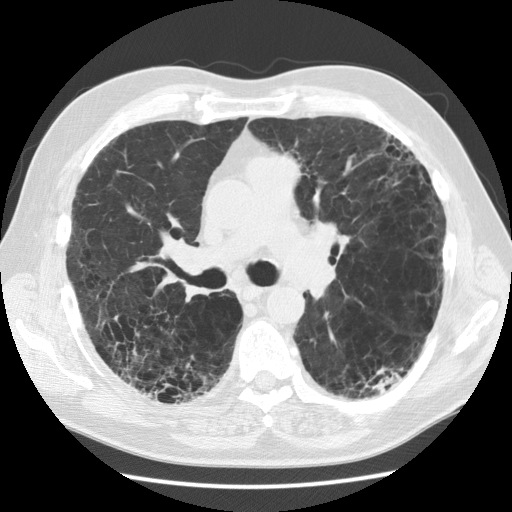
Low-dose screening chest CT, one axial slice. Slice 74 of 128 in the series (ordered by position). Reconstruction kernel STANDARD. 120 kVp. Lung window (W 1500 / L -600 HU). 2.5 mm slice thickness. 512 × 512 image matrix, field of view 360 × 360 mm.
Annotated regions visible in this slice (outlined manually by an expert reader):
- lesion 1 (tumor, lower lobe of left lung): box from (x=367, y=367) to (x=403, y=393) px